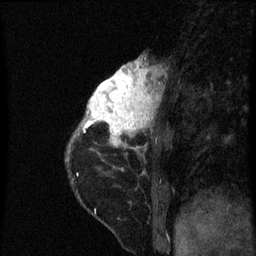
Breast MRI (dynamic contrast-enhanced), one sagittal slice. Position 19 of 60 along the scan axis. Dynamic contrast-enhanced series, image 2 of 3 at this slice position (ordered by acquisition). 1.5 T. TE 4.2 ms, TR 8 ms. 2 mm slice thickness. 256 × 256 image matrix. Patient: female, 38 years.
Outlined on this slice (semi-automatically segmented with operator editing):
- analysis volume of interest (the breast-tissue region the enhancement analysis was run in; not a lesion): bounding box [x1, y1, x2, y2] px = [80, 60, 163, 151]
- tumour enhancement mask (voxels above the 70 % enhancement threshold inside the analysis volume of interest): [84, 62, 159, 147]